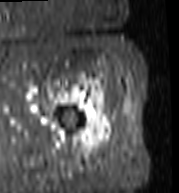
MRI of an extremity soft-tissue mass, one axial slice; position 90 of 103 along the scan axis; STIR; MR volume resampled by the dataset authors to the PET/CT grid (not the native acquisition matrix); 3.27 mm slice thickness; 179 × 193 image matrix, field of view 175 × 188 mm. Female patient. Case-level facts recorded for this patient, not image findings: histological type: undifferentiated – high grade; grade: high; site of the primary tumour: left thigh.
Outlined on this slice (expert contour drawn on MRI and transferred to this co-registered scan by the dataset authors):
- gross tumour volume including surrounding oedema: bounding box <68,76,112,156> (left, top, right, bottom; pixels)
- gross tumour volume (mass): <75,76,110,154>